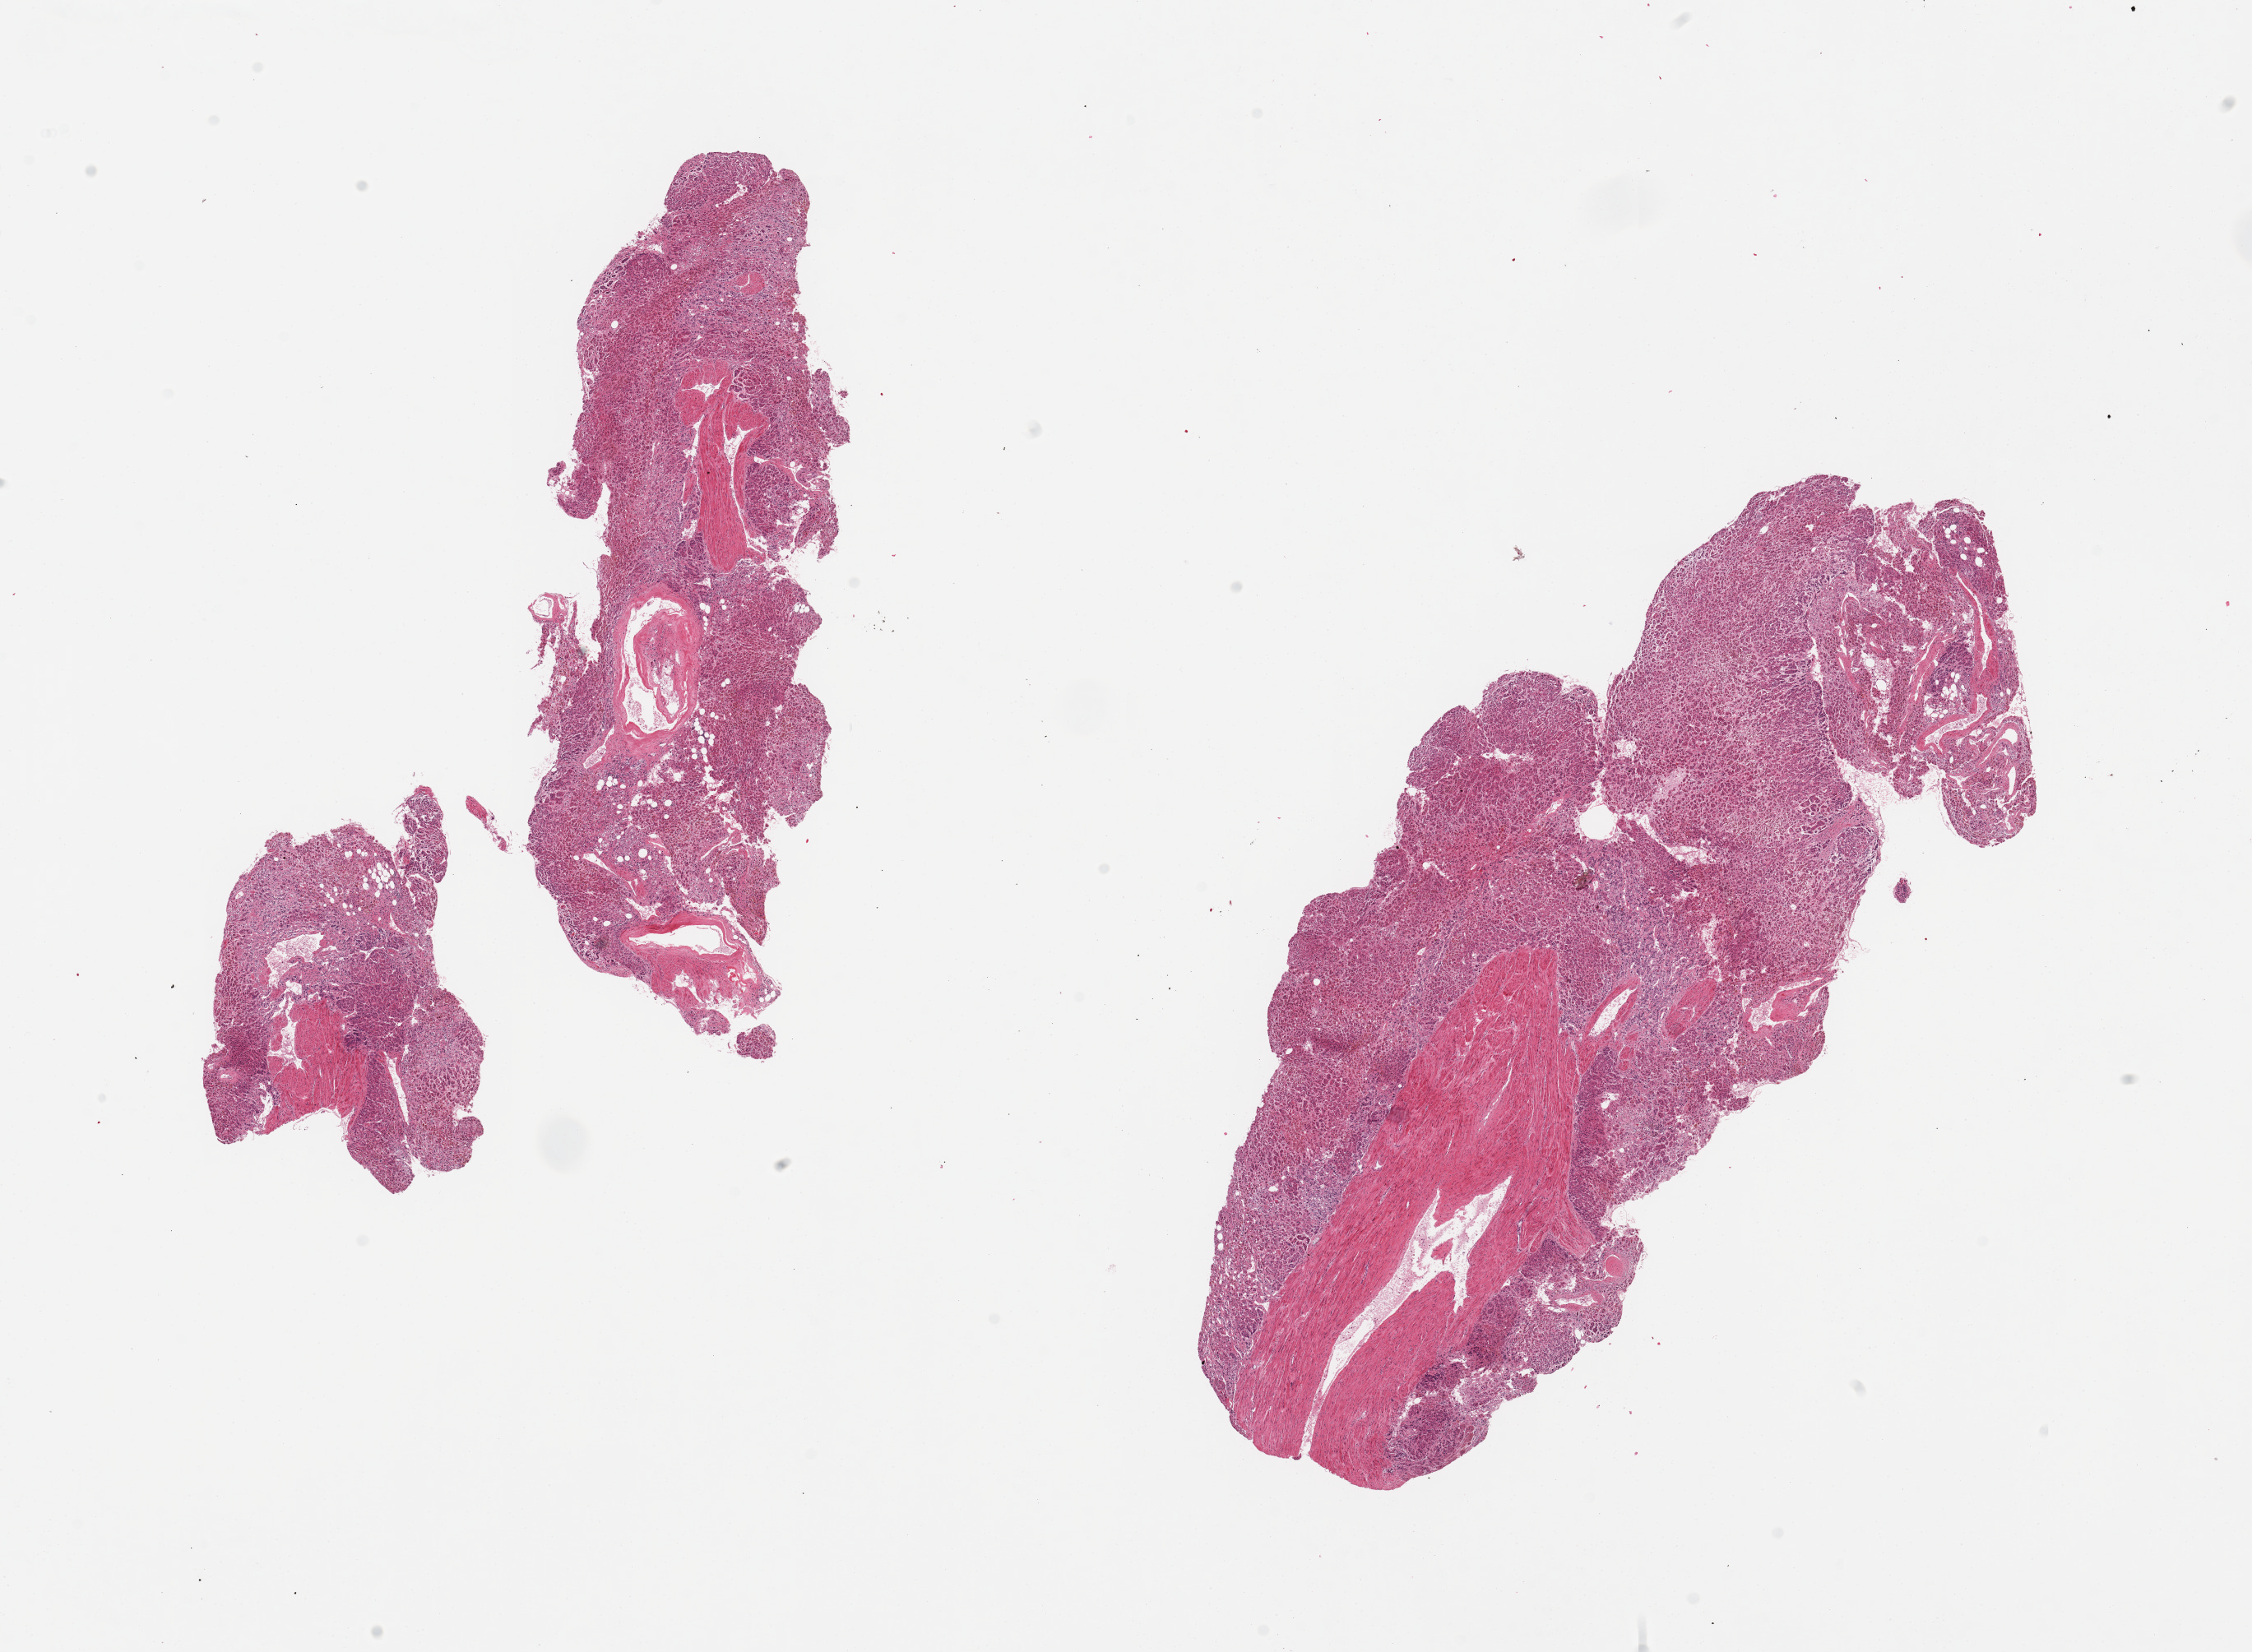
Hematoxylin and eosin (H&E) whole-slide image — whole scanned area (about 21.7 x 15.9 mm) shown as a low-resolution overview. PAXgene-fixed, paraffin-embedded tissue. Sampled site (target tissue): adrenal gland. Tissue donor sample. Donor sex: male.
* pathologist's review note for this sample: 3 pieces